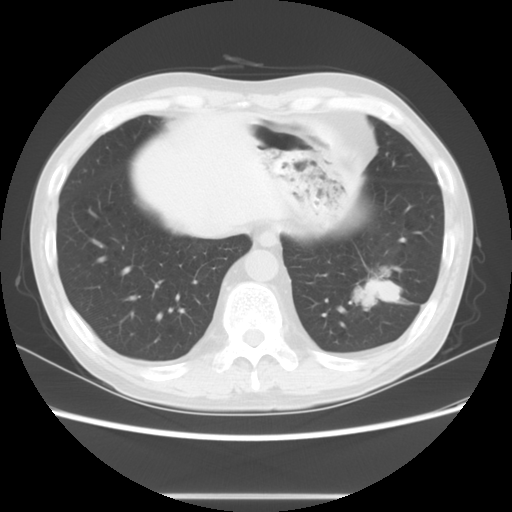
Chest CT, one axial slice; slice 21 of 63 in the series (ordered by position); 120 kVp; lung window (W 1500 / L -600 HU); 5 mm slice thickness; 512 × 512 image matrix, field of view 347 × 347 mm. Male patient, age 49 years. Case-level facts recorded for this patient, not image findings: clinical TNM (as recorded): T3 N0 M0; histopathological grade: G2-3.
Annotated regions visible in this slice (bounding box drawn by a radiologist):
- lung tumour (recorded histology: squamous cell carcinoma): box from (x=344, y=256) to (x=406, y=315) px